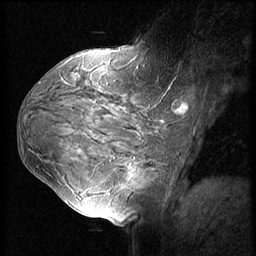
Breast MRI (dynamic contrast-enhanced), one sagittal slice. Slice 33 of 60 in the series (ordered by position). Dynamic contrast-enhanced series, image 2 of 3 at this slice position (ordered by acquisition). 1.5 T. TE 4.2 ms, TR 8.9 ms. 2.5 mm slice thickness. 256 × 256 image matrix, field of view 220 × 220 mm. Patient: female, 37 years. From the clinical record (not read from this slice): setting: breast cancer imaged before/during neoadjuvant chemotherapy; receptor status: triple-negative.
Annotated regions visible in this slice (semi-automatic segmentation, software-assisted and operator-edited):
- analysis volume of interest (the breast-tissue region the enhancement analysis was run in; not a lesion): bounding box [x1, y1, x2, y2] px = [114, 153, 159, 206]
- tumour enhancement mask (voxels above the 140 % enhancement threshold inside the analysis volume of interest): [130, 167, 137, 179]